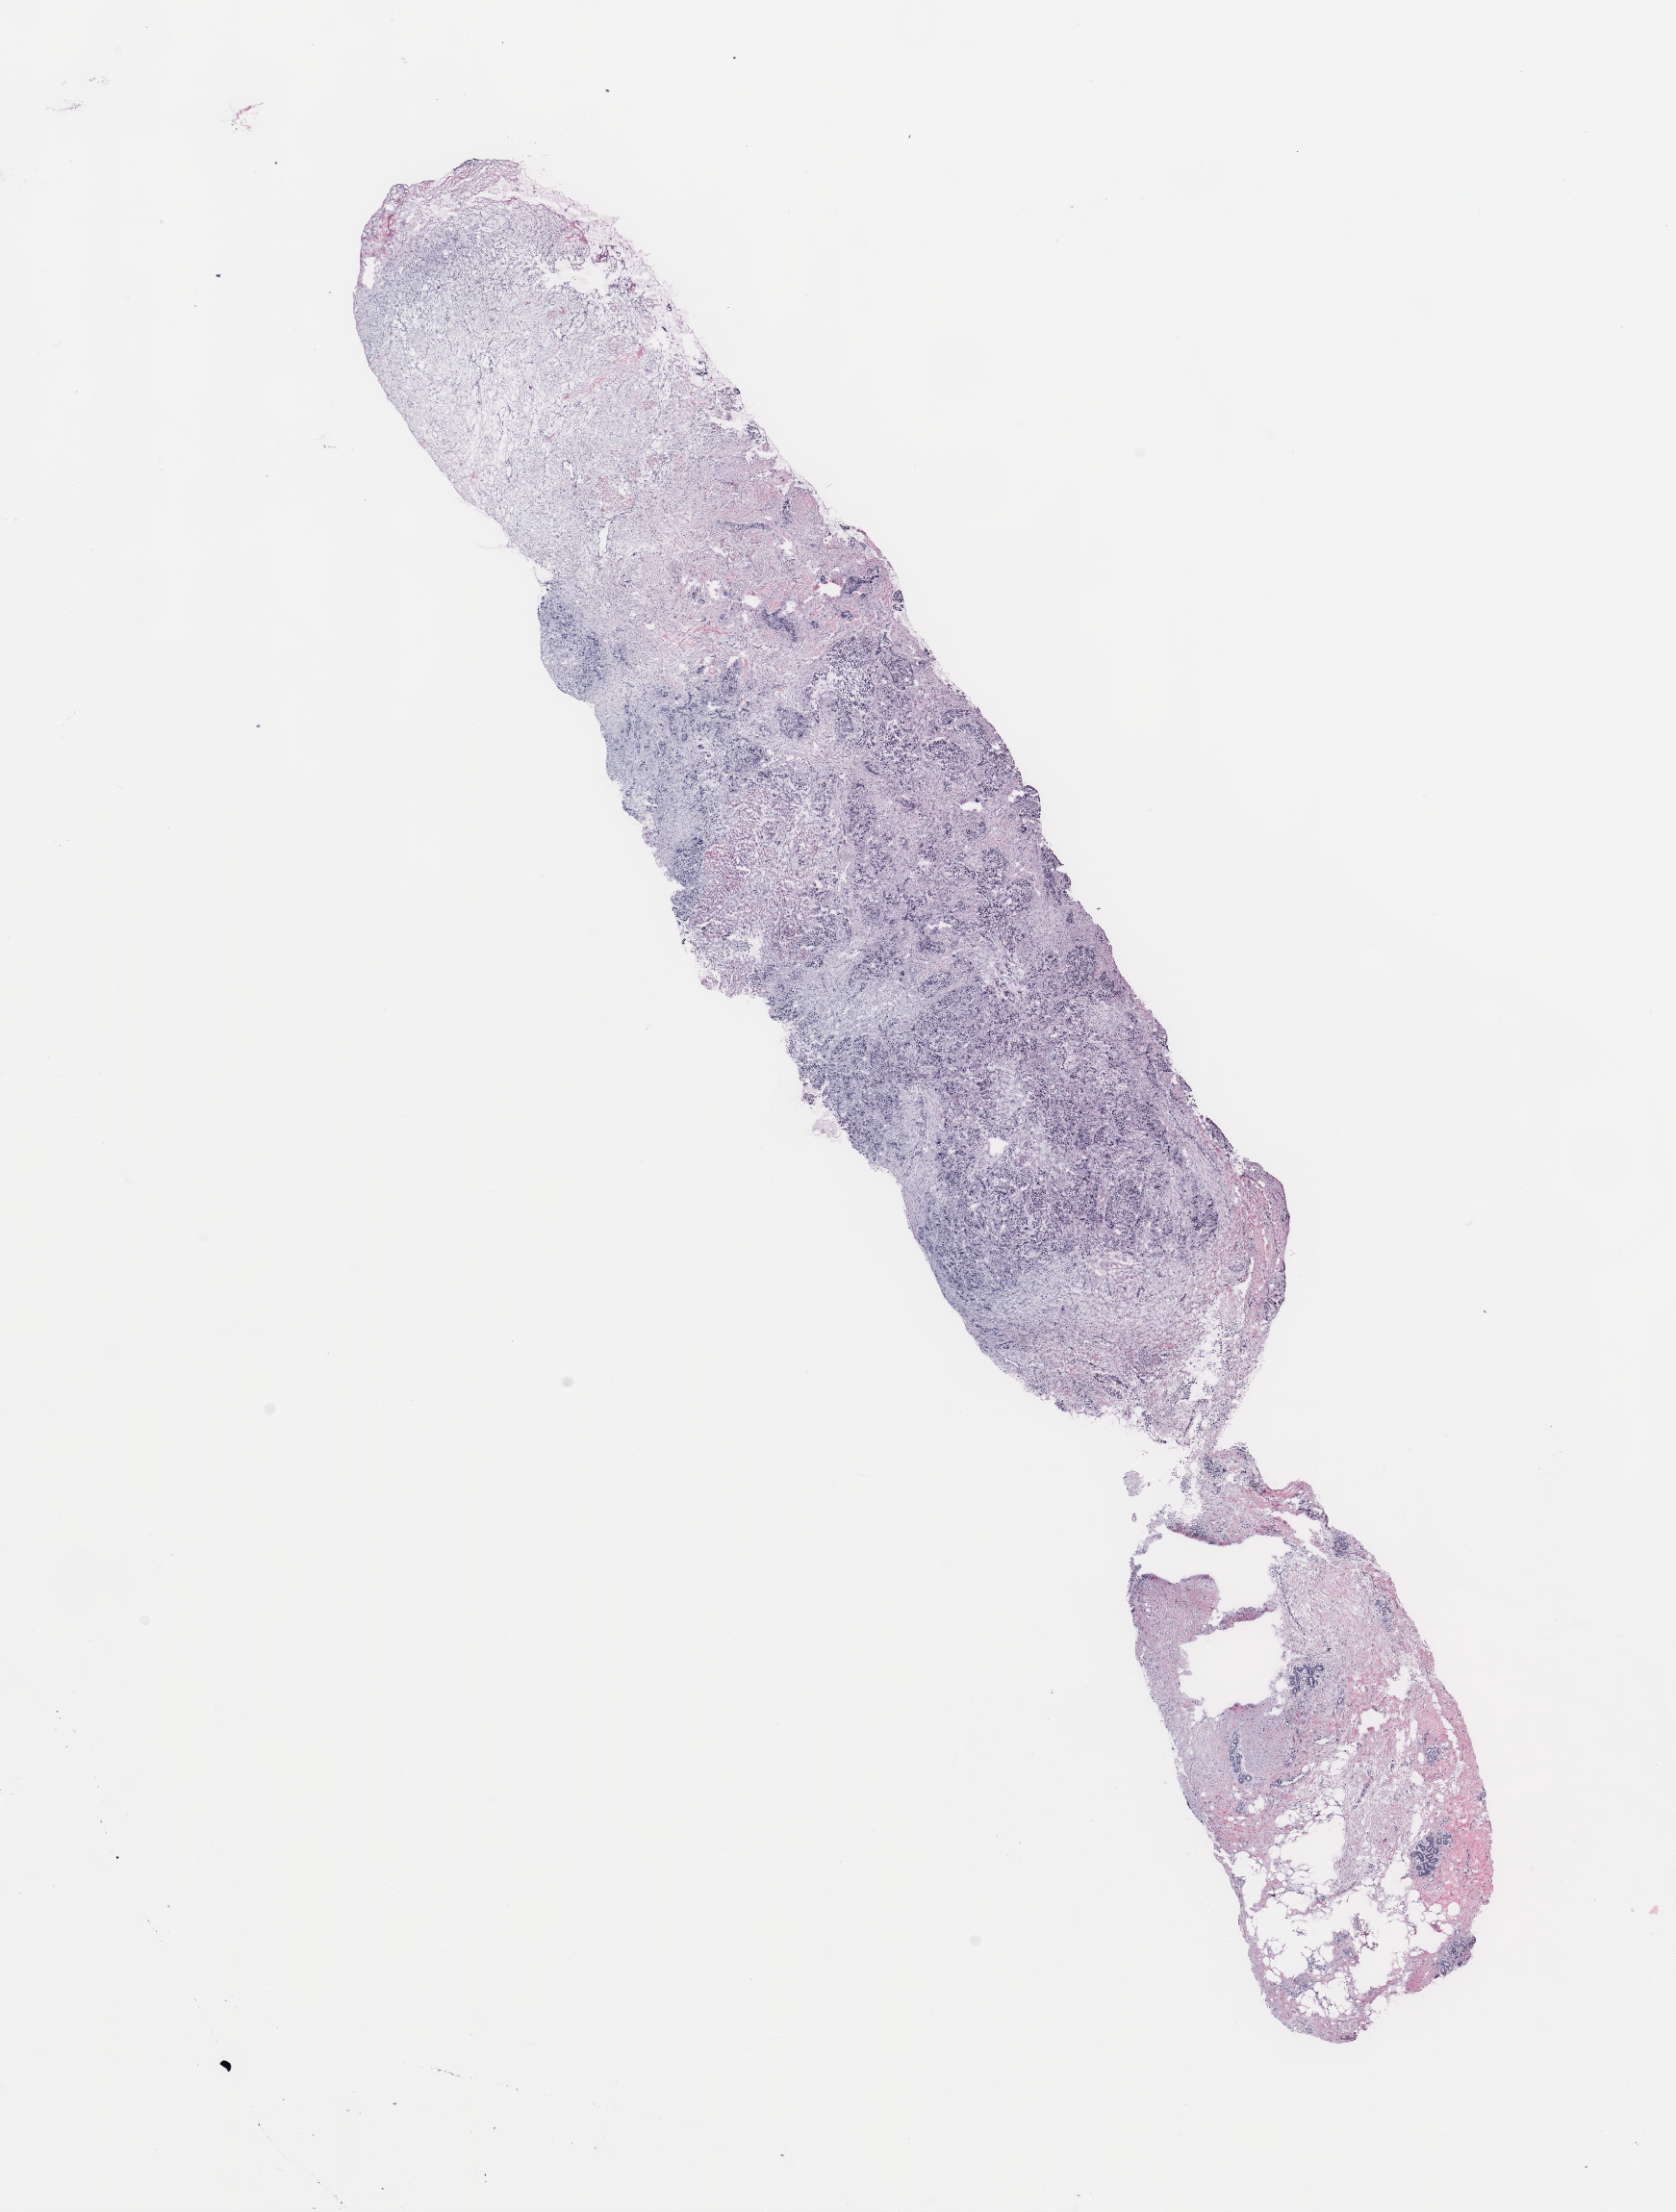
Digitized Hematoxylin and eosin (H&E) stained tissue section (whole slide), a low-resolution overview of the entire scanned area, about 13.8 x 18.2 mm (slide scanned at 20x). Female, 48 y/o.
- specimen: breast, tumour tissue